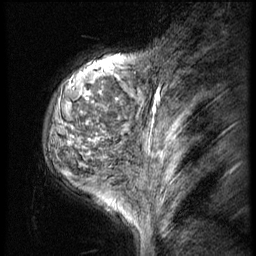
Breast MRI (dynamic contrast-enhanced), one sagittal slice; position 12 of 56 along the scan axis; 3 images stored at this slice position (order not interpretable as contrast timing); 1.5 T; TE 4.2 ms, TR 9 ms; 2.5 mm slice thickness; 256 × 256 image matrix, field of view 180 × 180 mm. Female patient, age 50 years. Case-level facts recorded for this patient, not image findings: setting: breast cancer imaged before/during neoadjuvant chemotherapy; receptor status: triple-negative.
Annotated regions visible in this slice (semi-automatically segmented with operator editing):
- analysis volume of interest (the breast-tissue region the enhancement analysis was run in; not a lesion): box from (x=42, y=50) to (x=135, y=191) px
- tumour enhancement mask (voxels above the 140 % enhancement threshold inside the analysis volume of interest): (x=68, y=88)–(x=88, y=144)